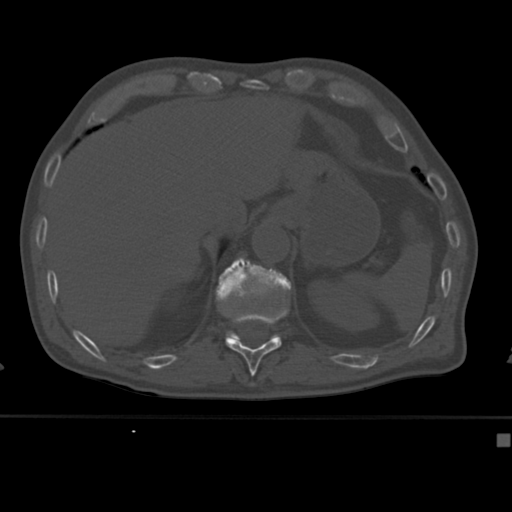
CT including the spine, one axial slice. Position 204 of 430 along the scan axis. 120 kVp. Bone window (W 1800 / L 400 HU). 512 × 512 image matrix. Male patient, age 64 years. Case-level facts recorded for this patient, not image findings: primary cancer: uterus; vertebrae with lytic lesions (as recorded): T1, T4, T5, T7, L5.
Structures marked on this image (semi-automatically segmented with operator editing):
- T11 vertebra: bounding box (x1, y1, x2, y2) in pixels: (220, 304, 289, 376)
- T12 vertebra: (215, 257, 292, 339)